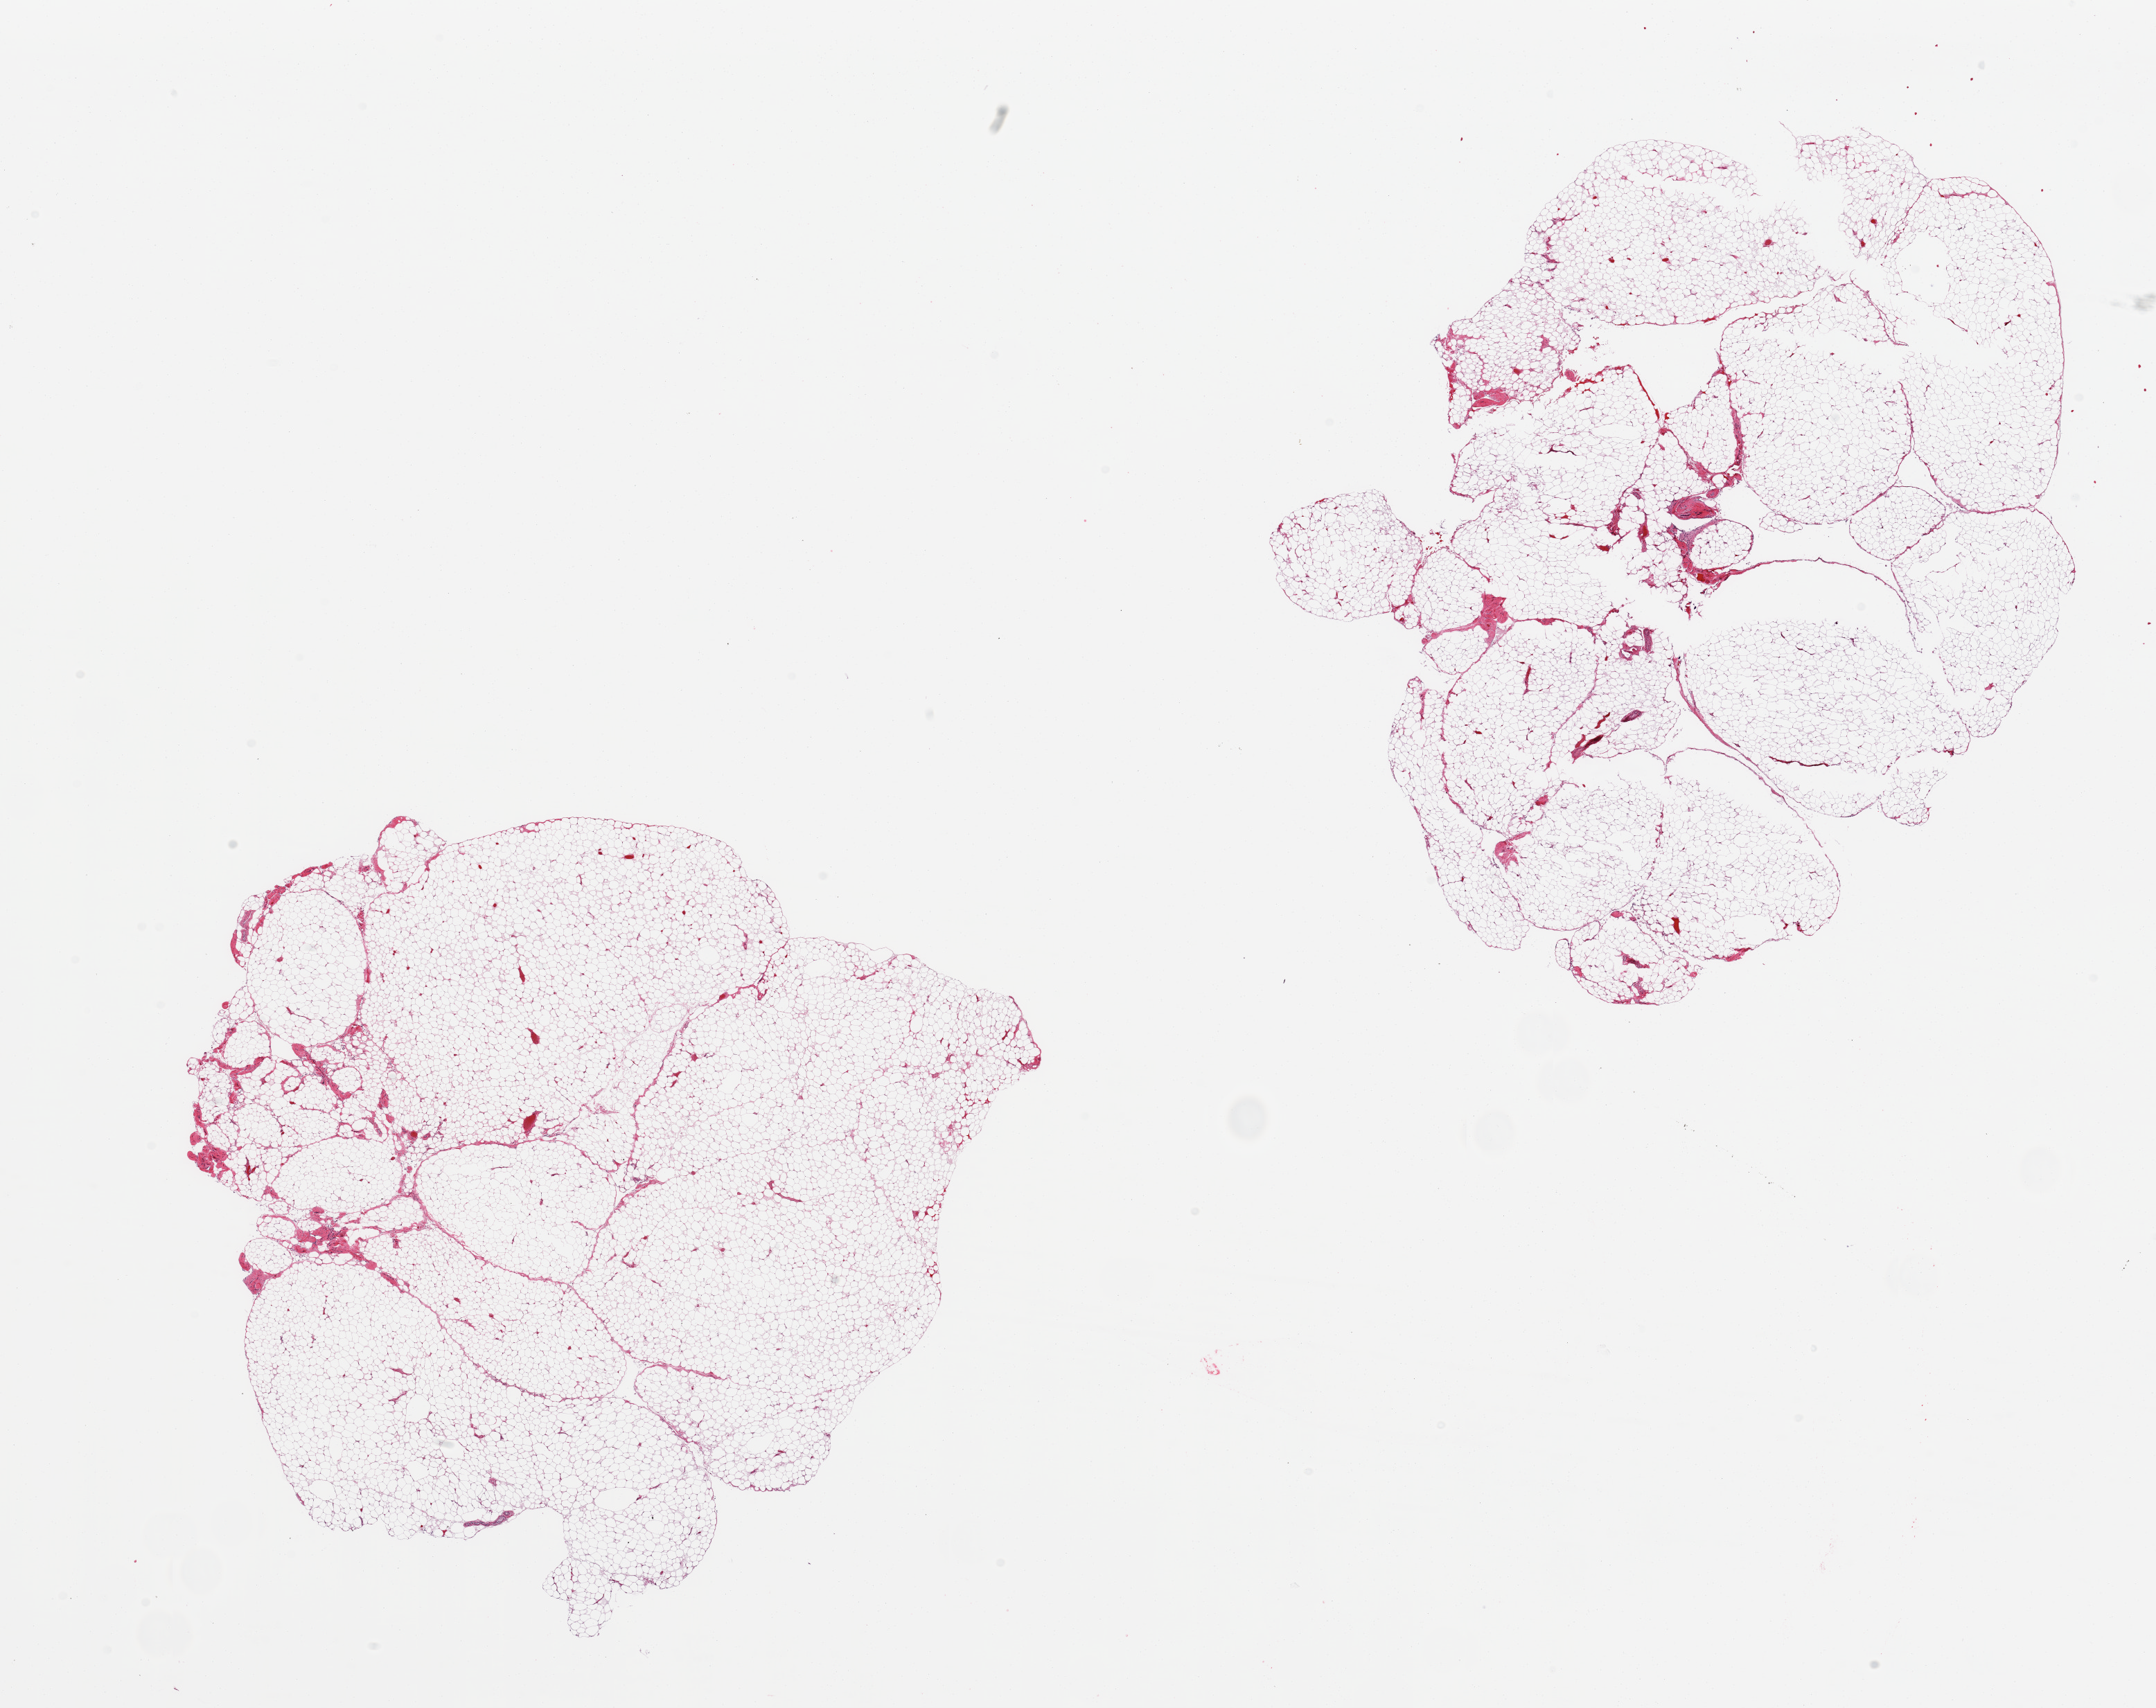
Whole-slide image, haematoxylin and eosin stain, brightfield, shown as a low-resolution overview of the whole scanned area (about 24.6 x 19.5 mm, slide scanned at 20x); PAXgene-fixed, paraffin-embedded tissue; section of omentum (target tissue); tissue donor sample.
Reviewer comment on this tissue sample: 2 pieces; mature adipose tissue.